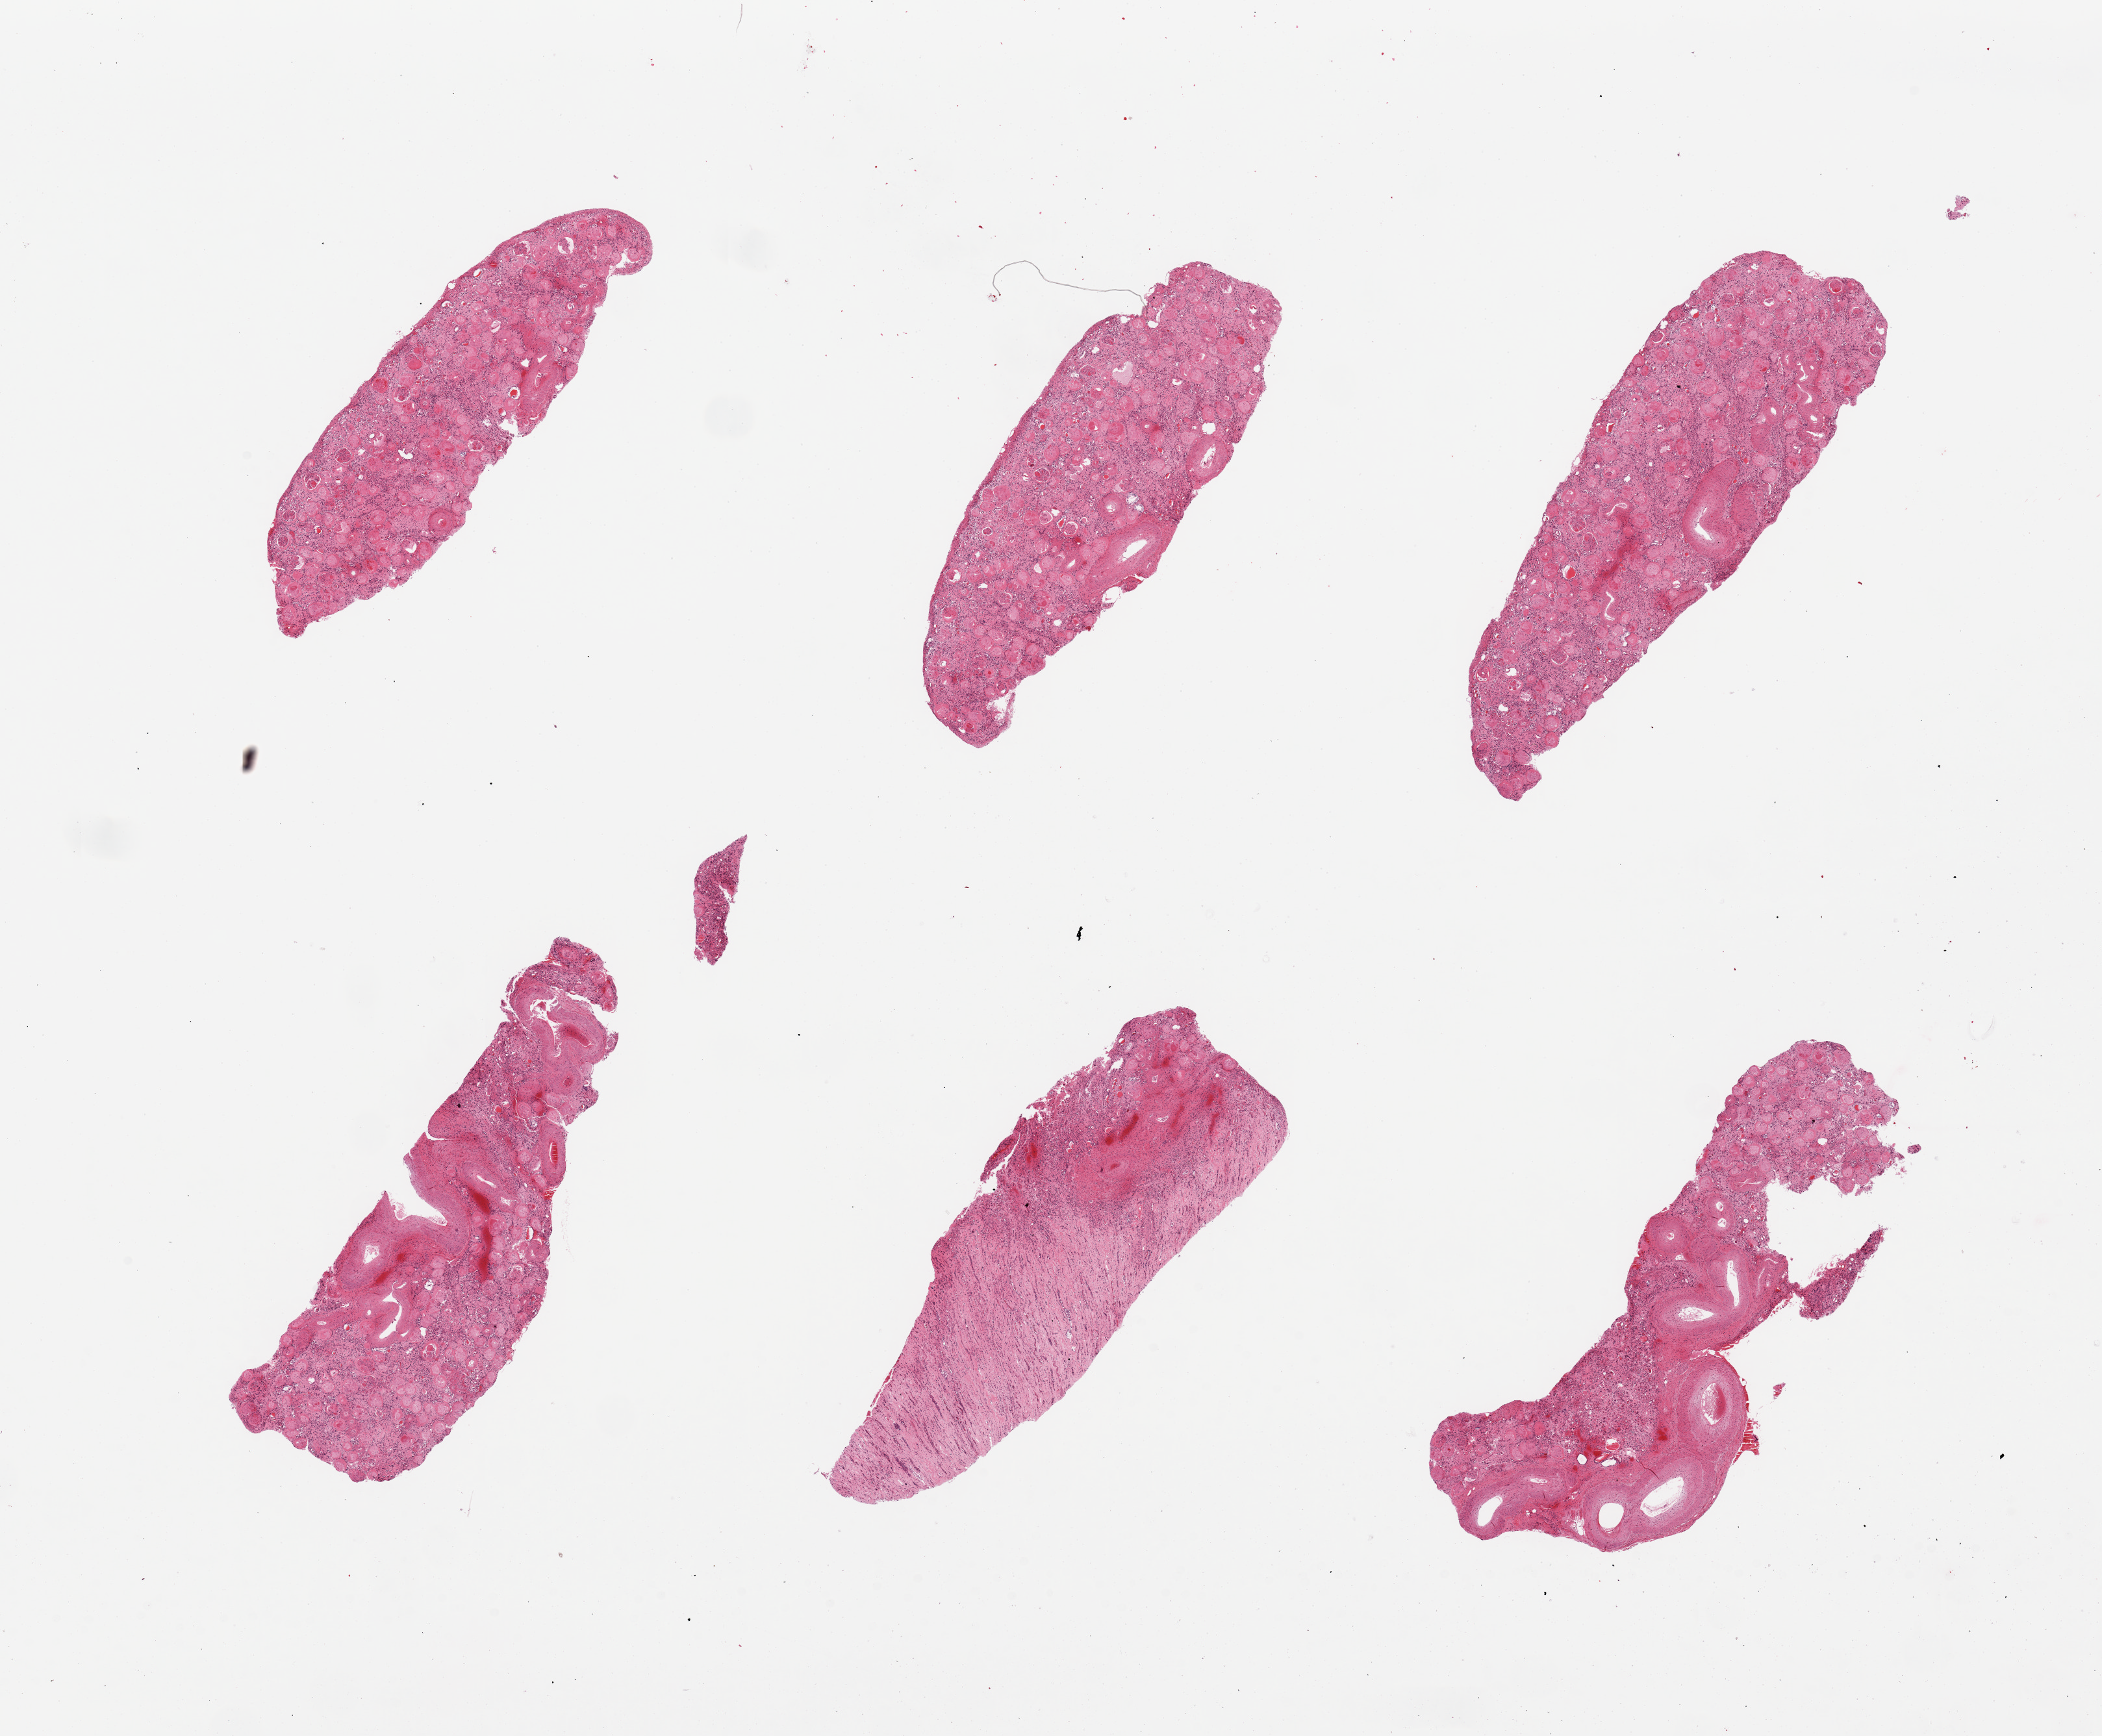
Haematoxylin and eosin whole-slide image, a low-resolution overview of the entire scanned area, about 25.6 x 21.1 mm, PAXgene-fixed, paraffin-embedded tissue, section of renal cortex (target tissue), tissue donor sample. Donor: female.
* review note (as recorded): 6 pieces, diffuse and nodular glomerulosclerosis, arteriolosclerosis, fibrosis, renal medulla also present